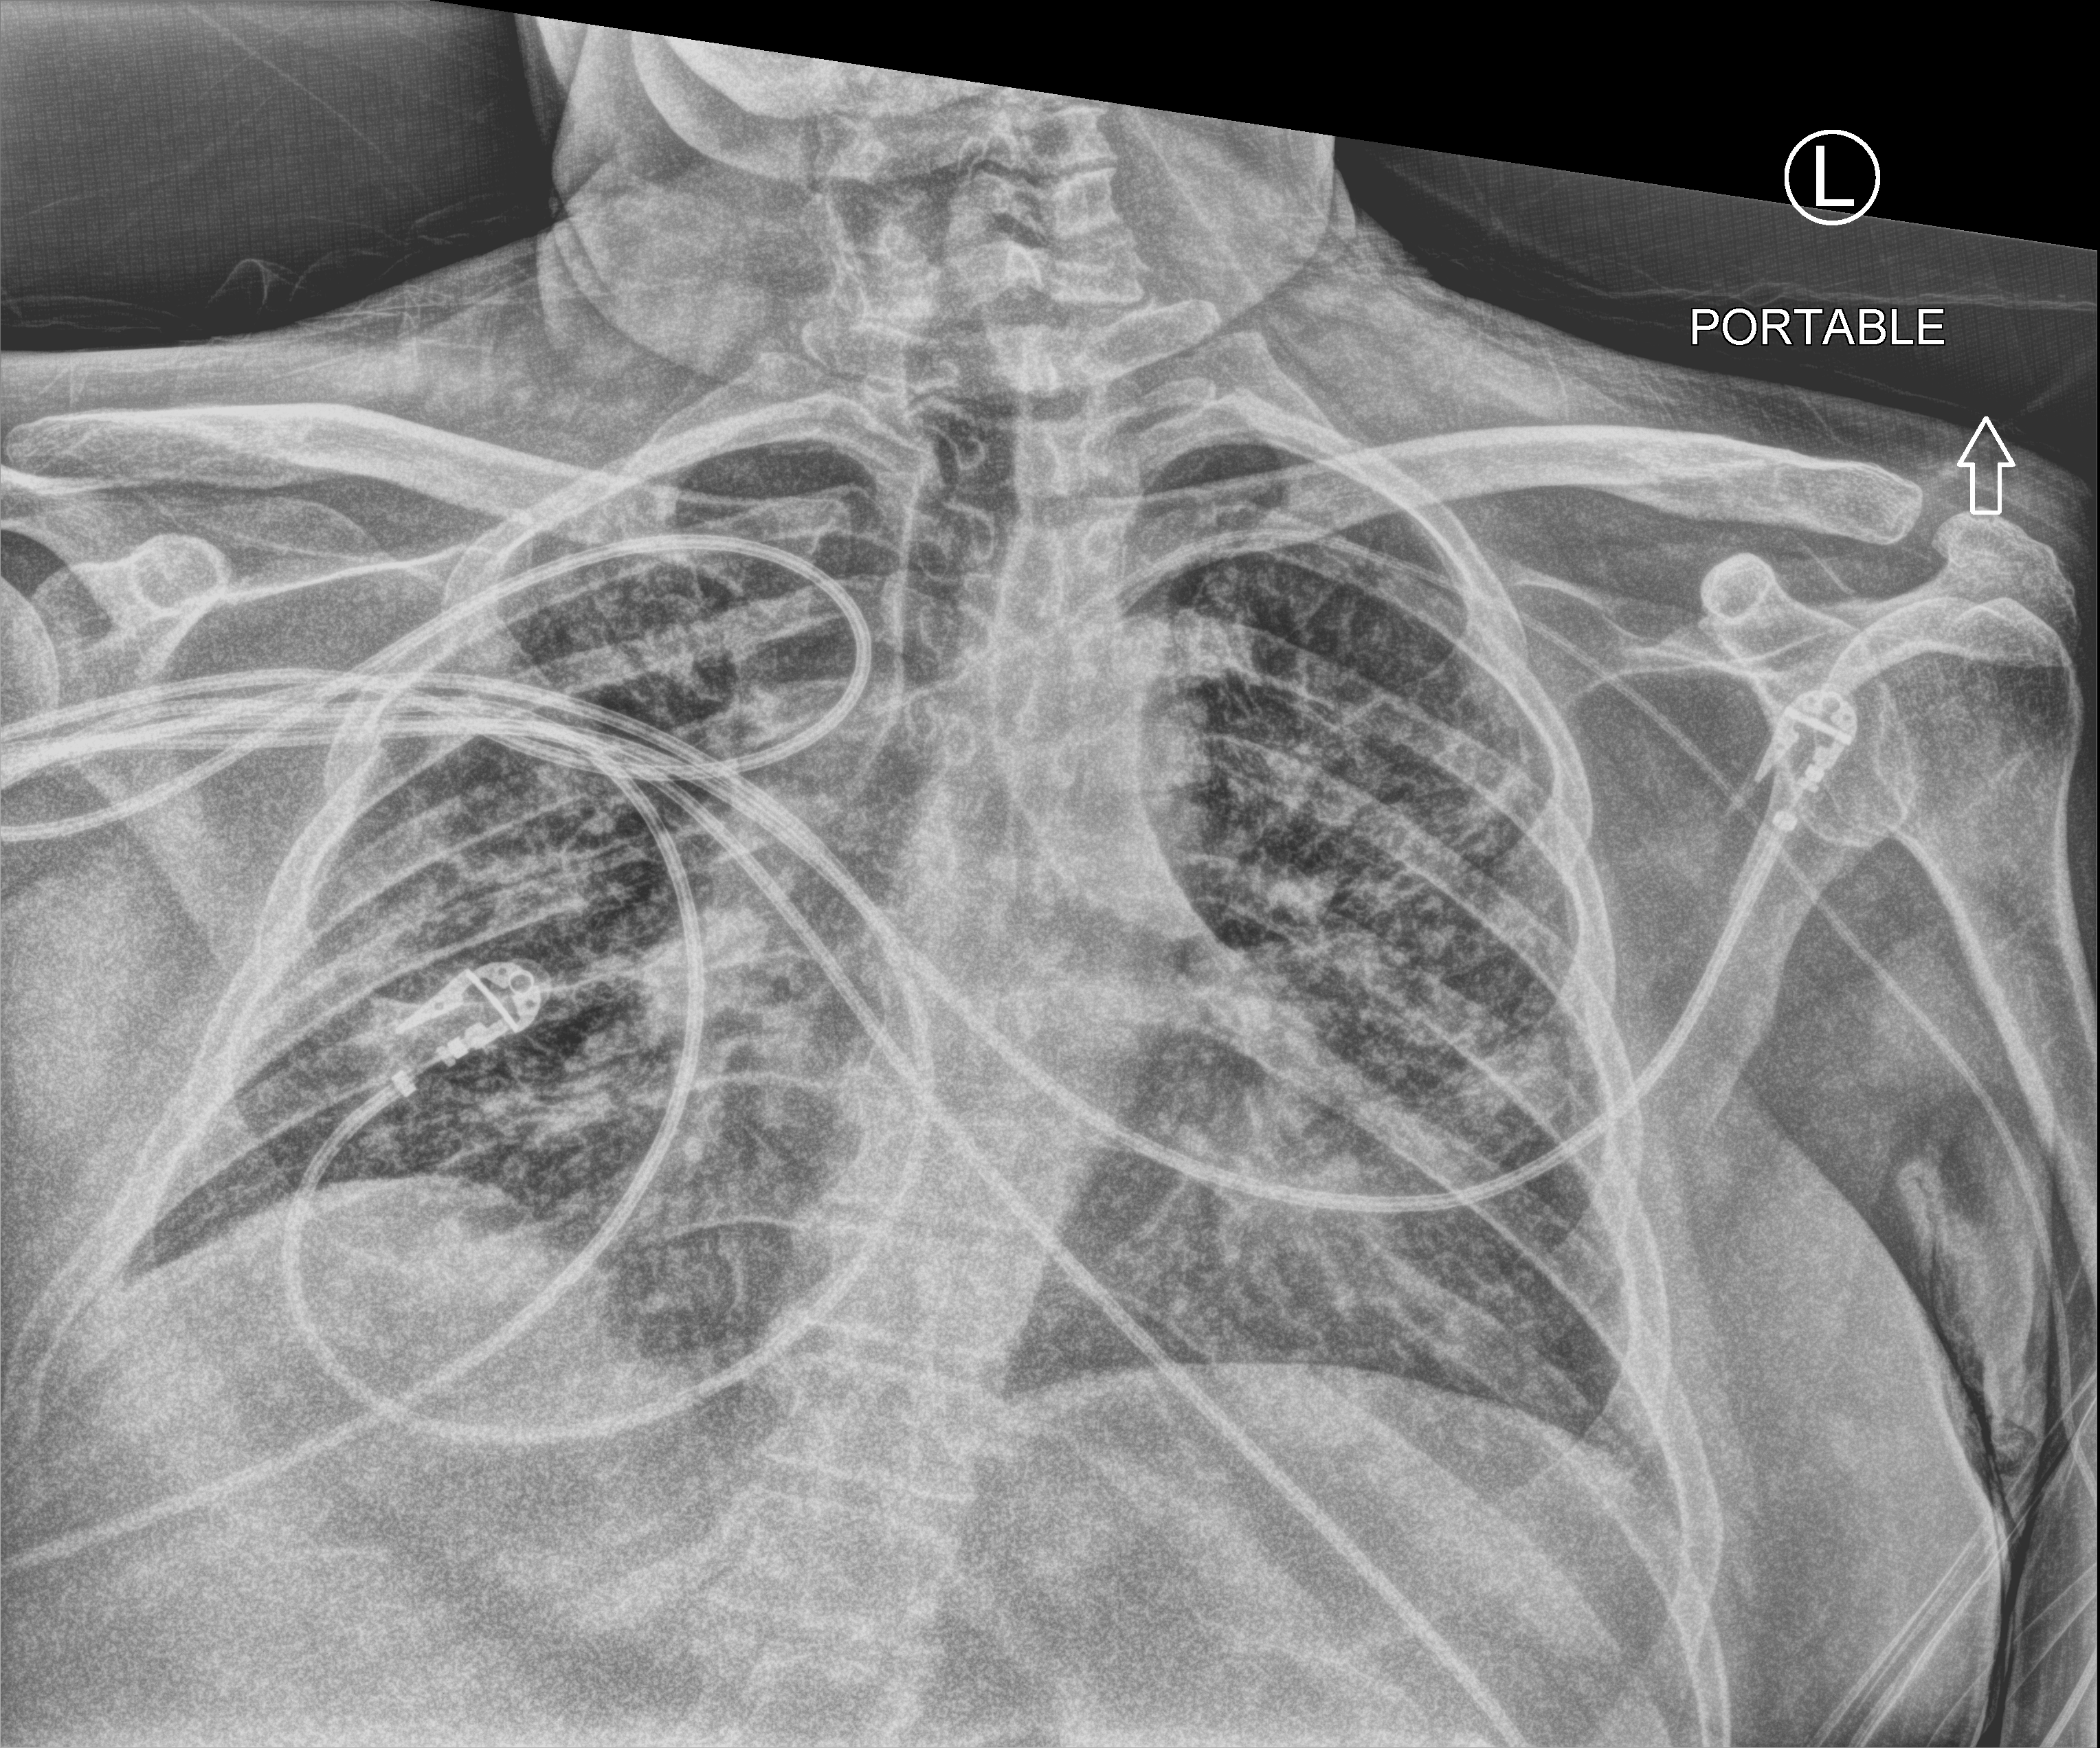
Chest X-ray (portable). Male patient hospitalised with COVID-19, age 18–59 years.
Admission-level facts for this patient (not findings on this image; timing relative to this image not recorded):
- length of hospital stay: 39 days
- chronic kidney disease (admission record): no
- admitted to intensive care during this hospital stay: yes